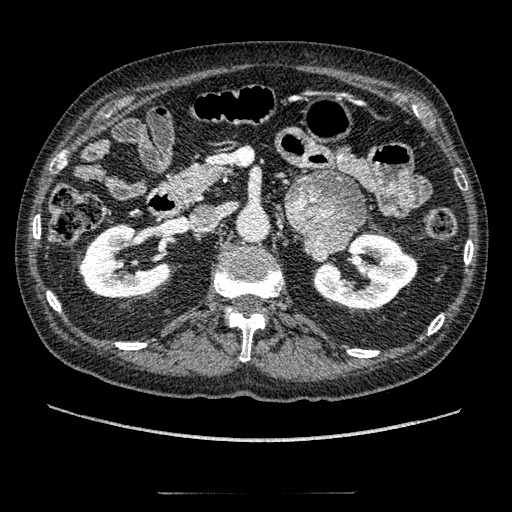
Contrast-enhanced abdominal CT, one axial slice; slice 104 of 274 in the series (ordered by position); reconstruction kernel STANDARD; 120 kVp; intravenous contrast given; soft-tissue window (W 400 / L 40 HU); 512 × 512 image matrix, field of view 381 × 381 mm. Male patient, age 69 years. Case-level facts recorded for this patient, not image findings: diagnosis: adrenocortical carcinoma; tumour side: left adrenal; tumour size at pathology: 6.1 cm; Ki-67 index: 10 %; stage (as recorded): 3.
Structures marked on this image (semi-automatically segmented with operator editing):
- mass: box from (x=286, y=172) to (x=365, y=258) px